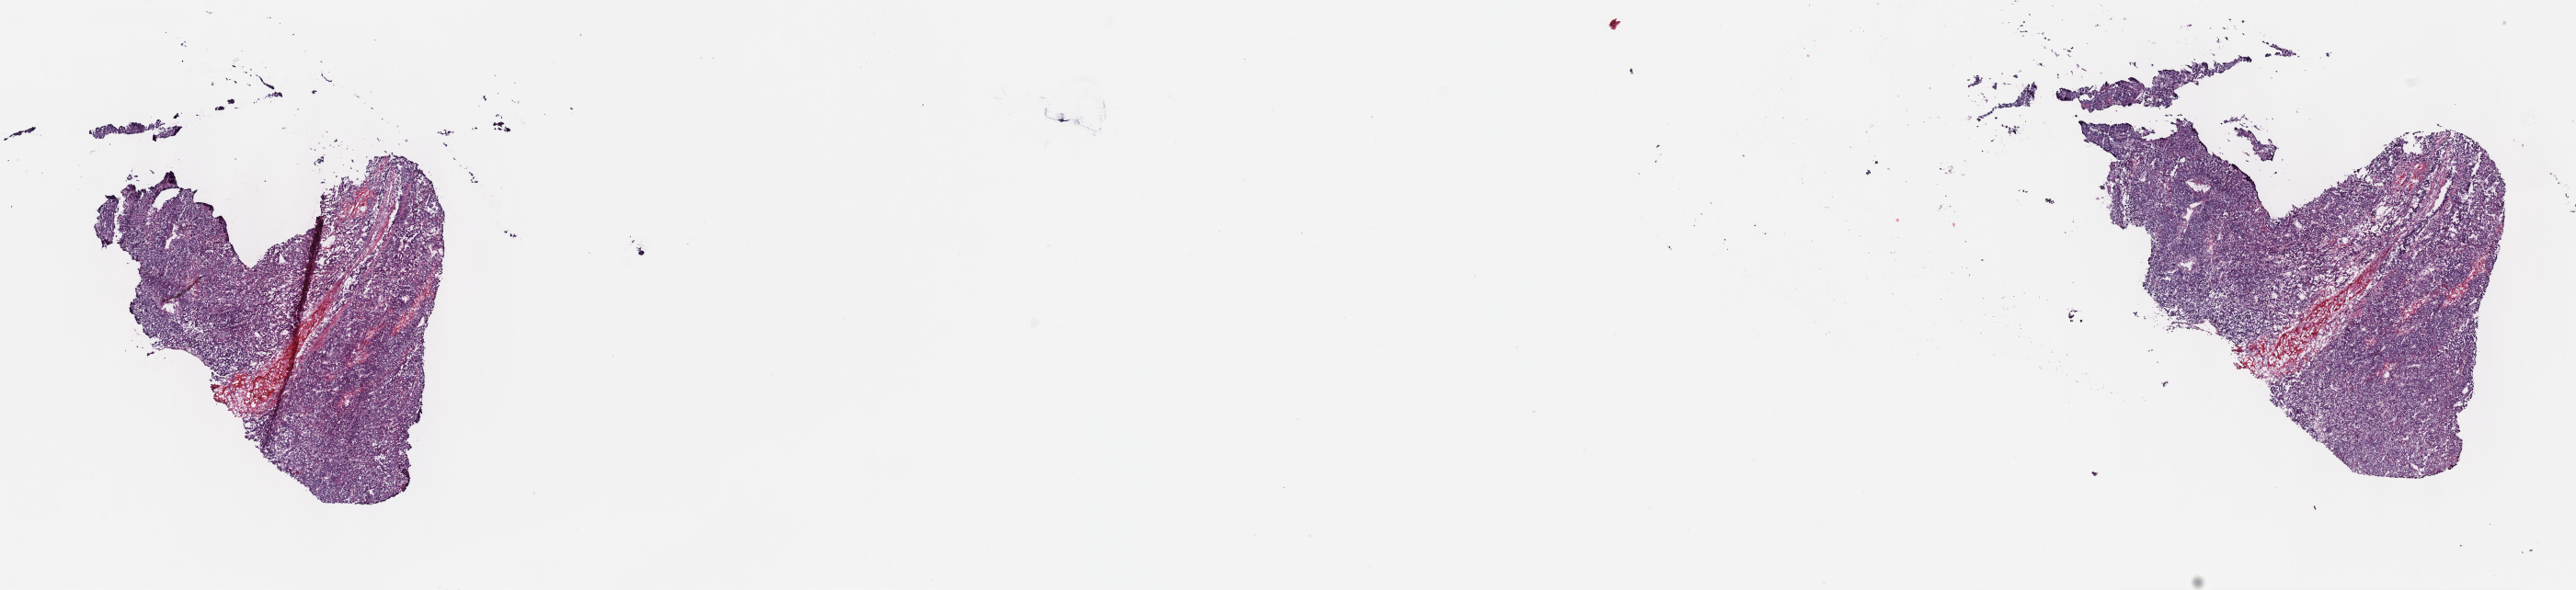
Digitized Hematoxylin and eosin (H&E) stained tissue section (whole slide), a low-resolution overview of the entire scanned area, about 22.7 x 5.2 mm (from a 40x scan), frozen section, sample: primary tumour, liver. Male patient; age at initial diagnosis 56 years. Histologic grade: G2 (moderately differentiated). Slide review estimates, as recorded: tumour cells 85%, tumour nuclei 90%, normal cells 0%, stromal cells 15%, necrosis 0%. Infiltration values recorded for this section: lymphocyte infiltration 0%, monocyte infiltration 0%, neutrophil infiltration 0%.
AJCC pathologic stage: IIIA. Histologic diagnosis: Hepatocellular carcinoma, NOS.